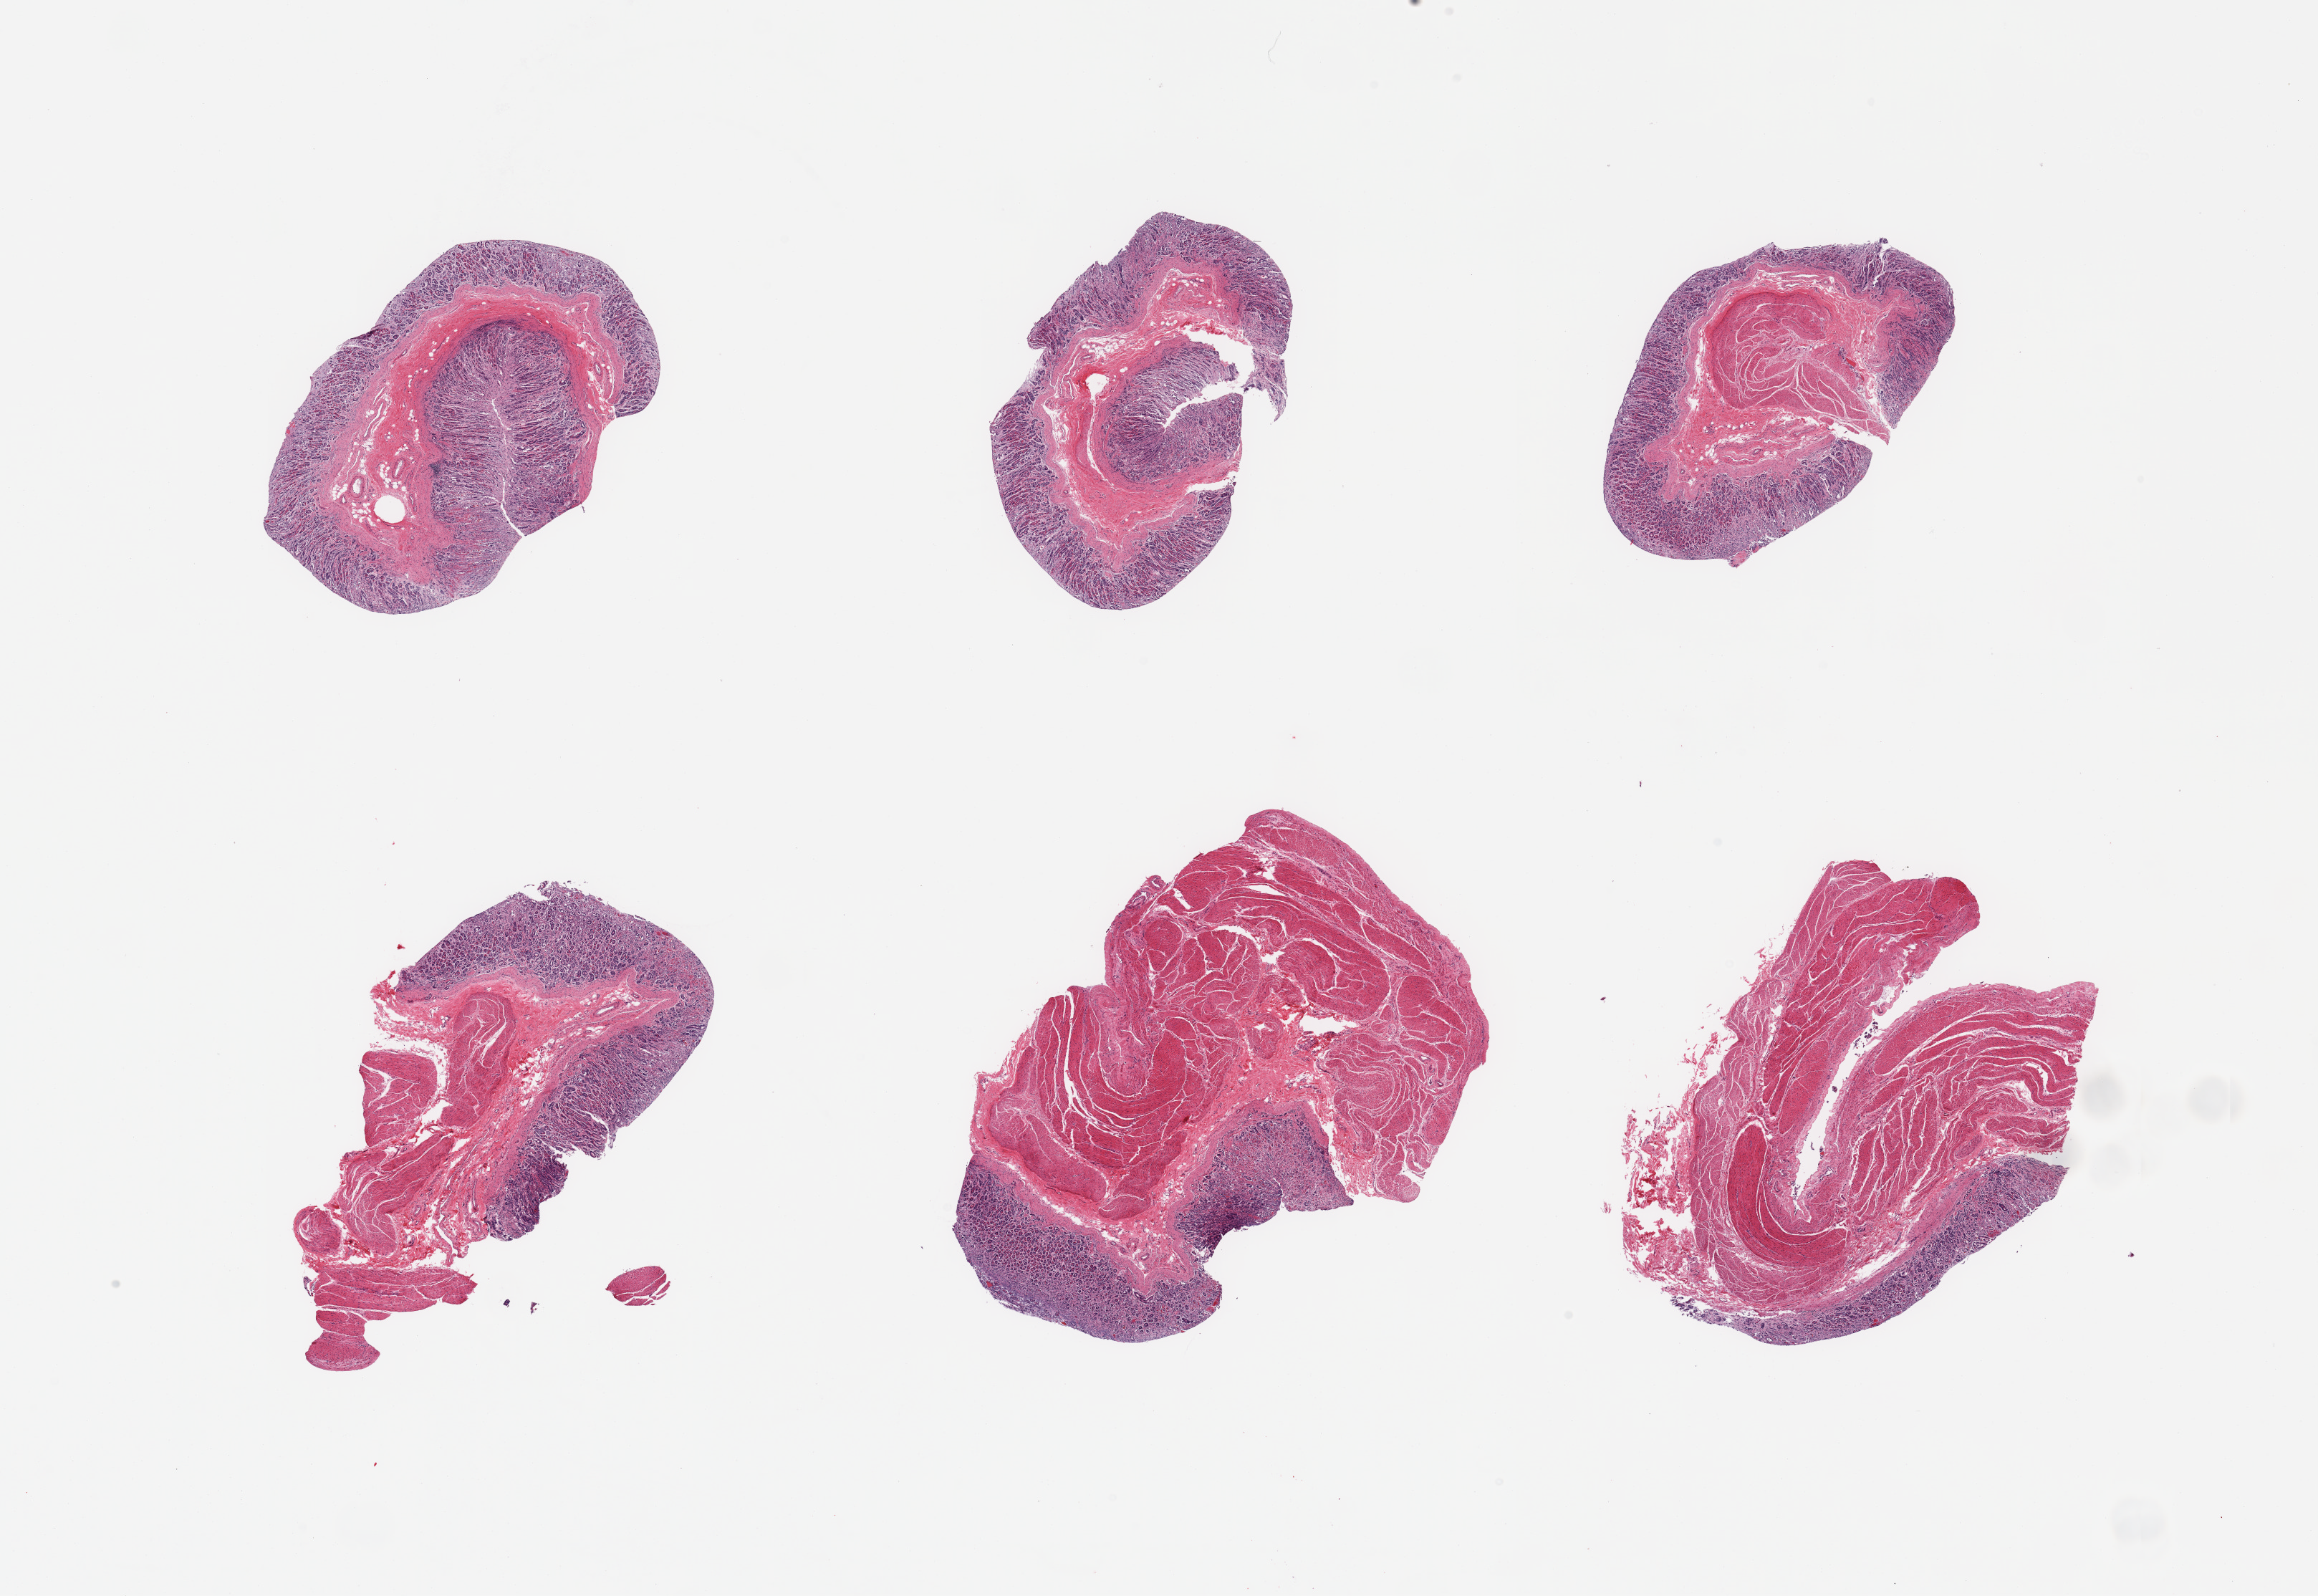
Digitized haematoxylin and eosin-stained section, a low-resolution overview of the entire scanned area, about 25.6 x 17.6 mm (from a 20x scan). PAXgene-fixed paraffin-embedded (PFPE) section. Target tissue: stomach. Tissue donor sample. Donor sex: male.
Review note (as recorded): 6 pieces: 2 without muscularis; chronic gastritis.